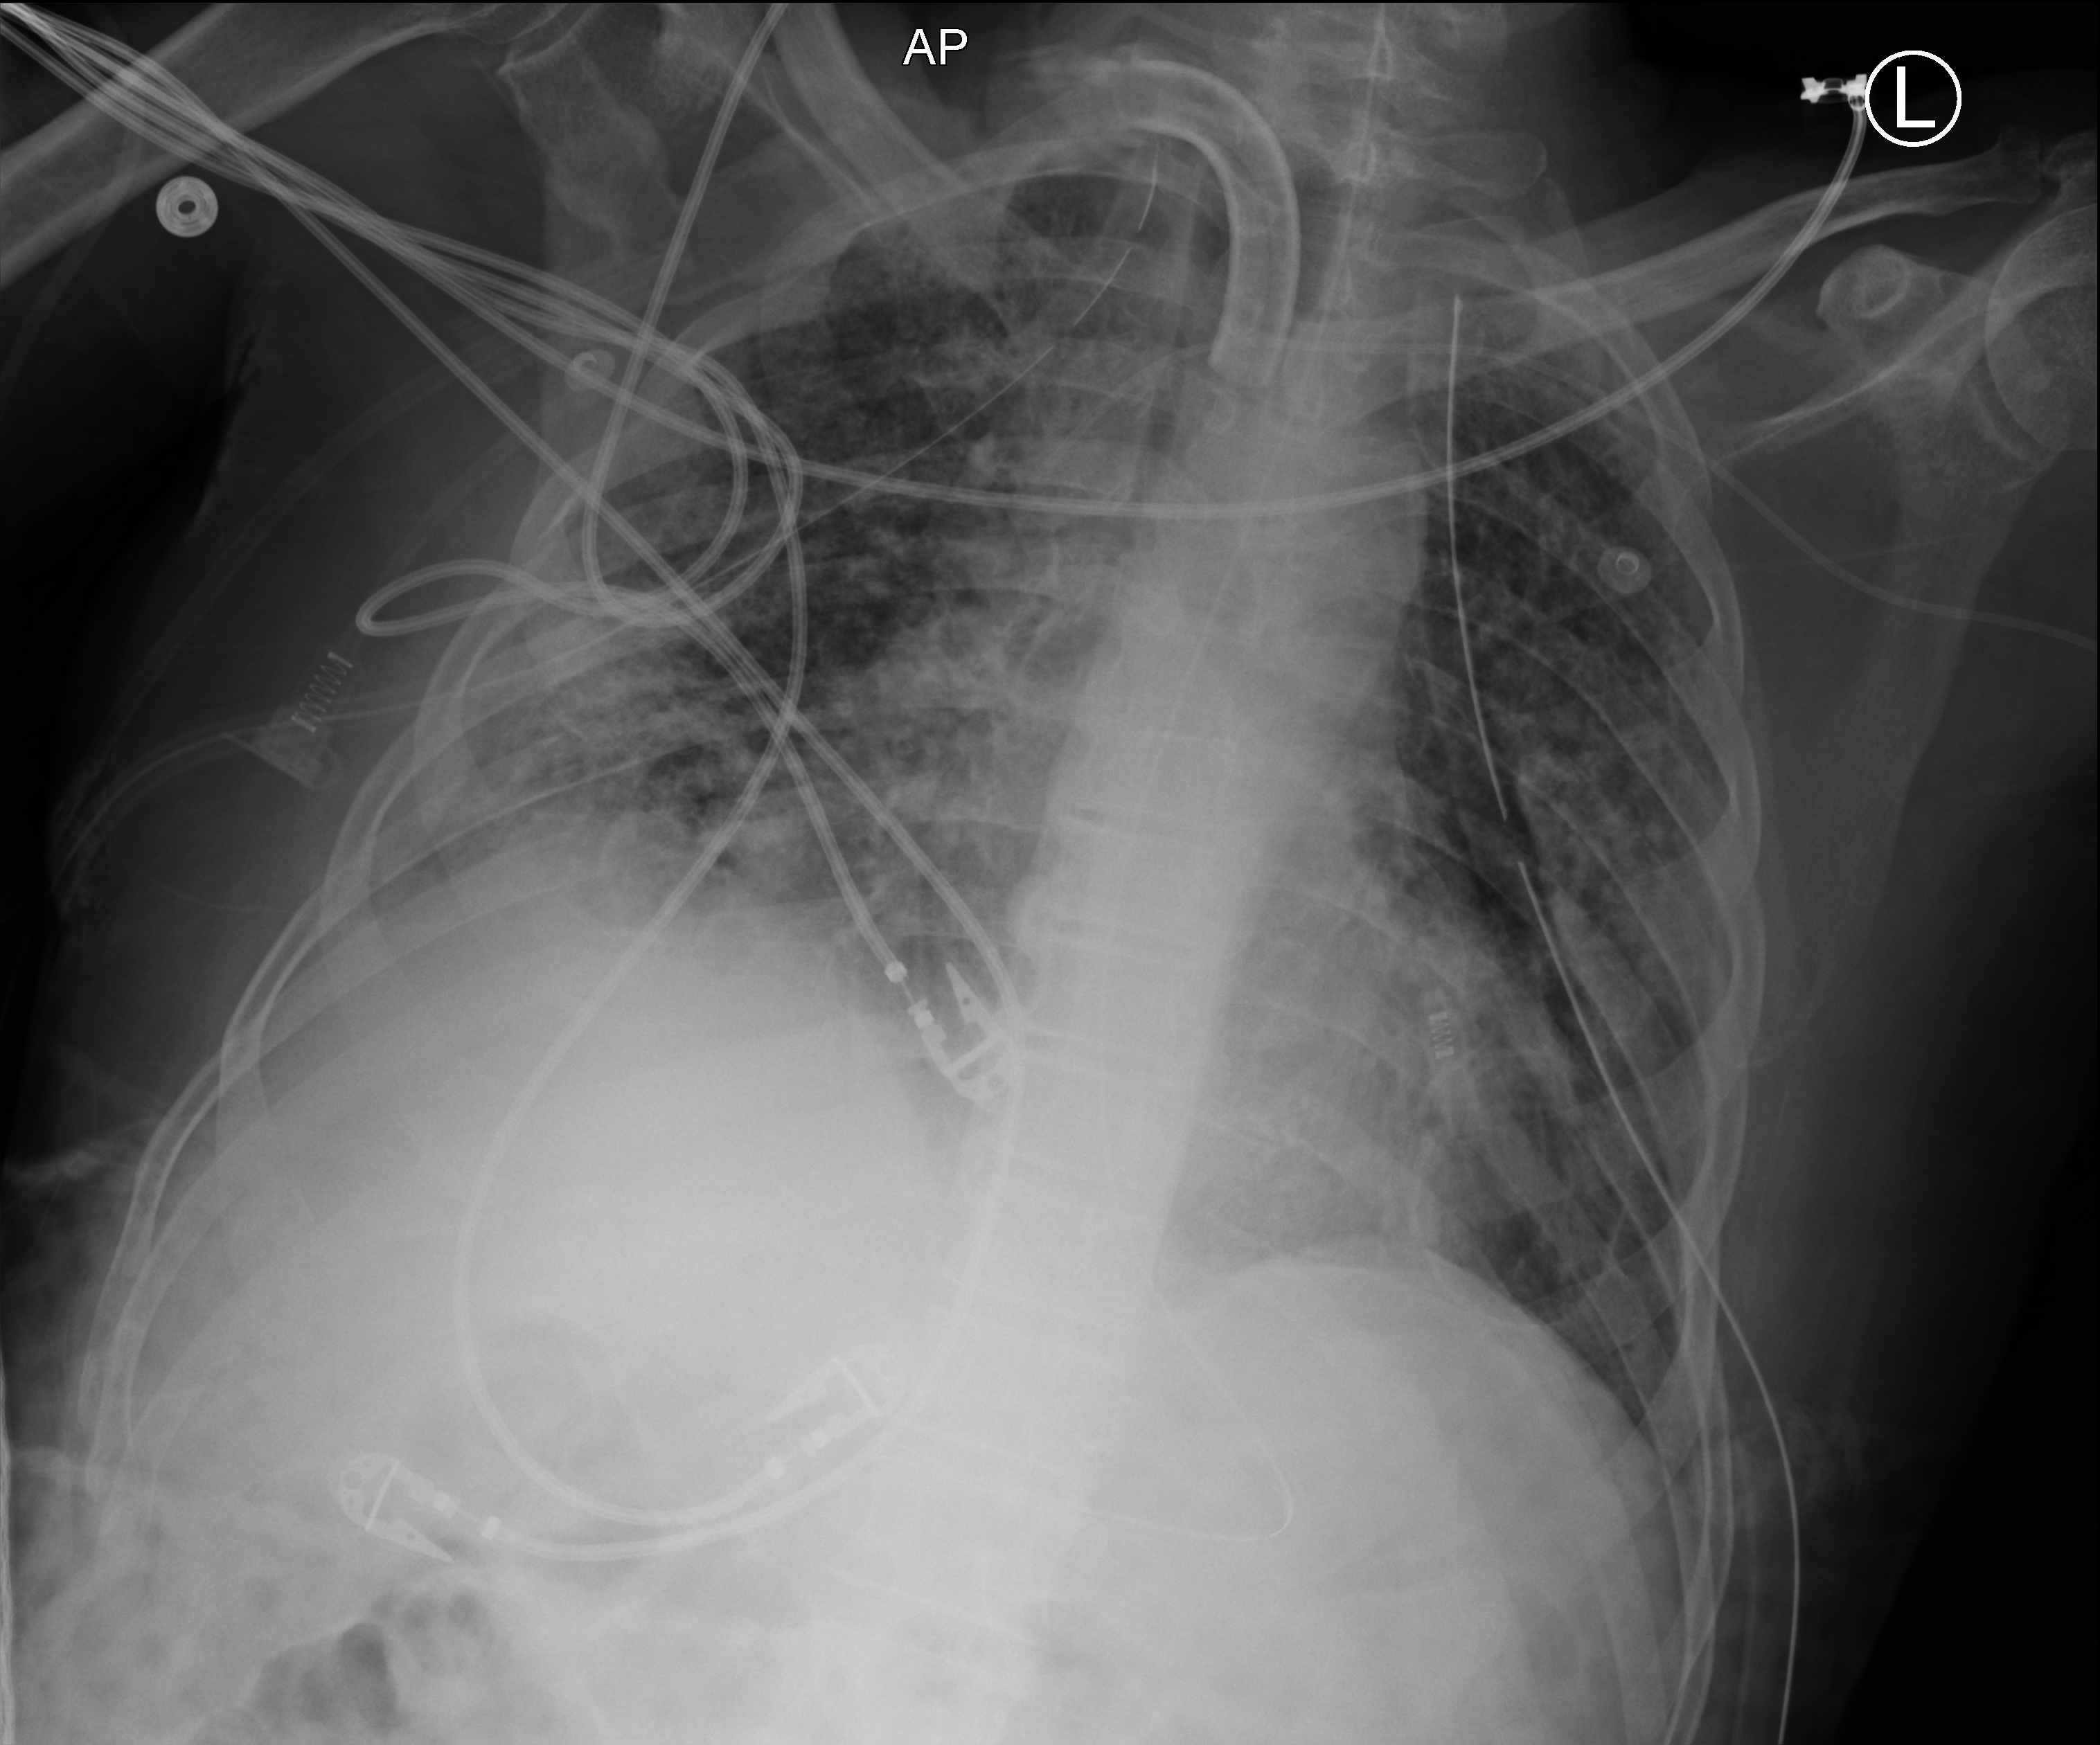
Portable chest radiograph. Male patient hospitalised with COVID-19, age 18–59 years.
From the hospital-stay record, not from the radiograph (when in the stay this image was taken is not recorded):
- admitted to intensive care during this hospital stay: yes
- other chronic lung disease (admission record): no